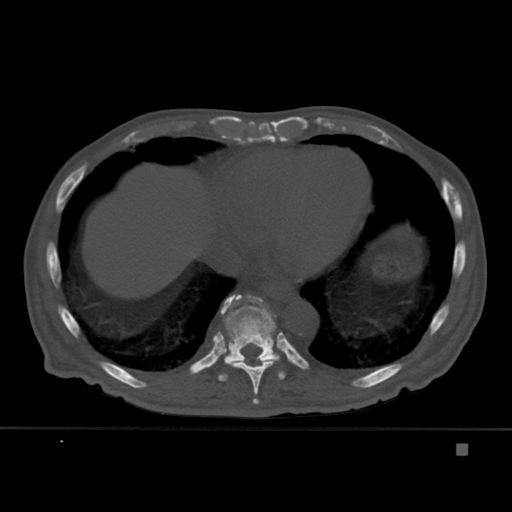
CT including the spine, one axial slice. Slice 240 of 451 in the series (ordered by position). Bone window (W 1800 / L 400 HU). 1.5 mm slice thickness. 512 × 512 image matrix, field of view 378 × 378 mm. Male patient, age 75 years. Case-level facts recorded for this patient, not image findings: primary cancer: prostate.
Structures marked on this image (semi-automatic segmentation, software-assisted and operator-edited):
- T10 vertebra: bounding box (x1, y1, x2, y2) in pixels: (213, 295, 286, 382)
- T9 vertebra: (219, 298, 281, 405)